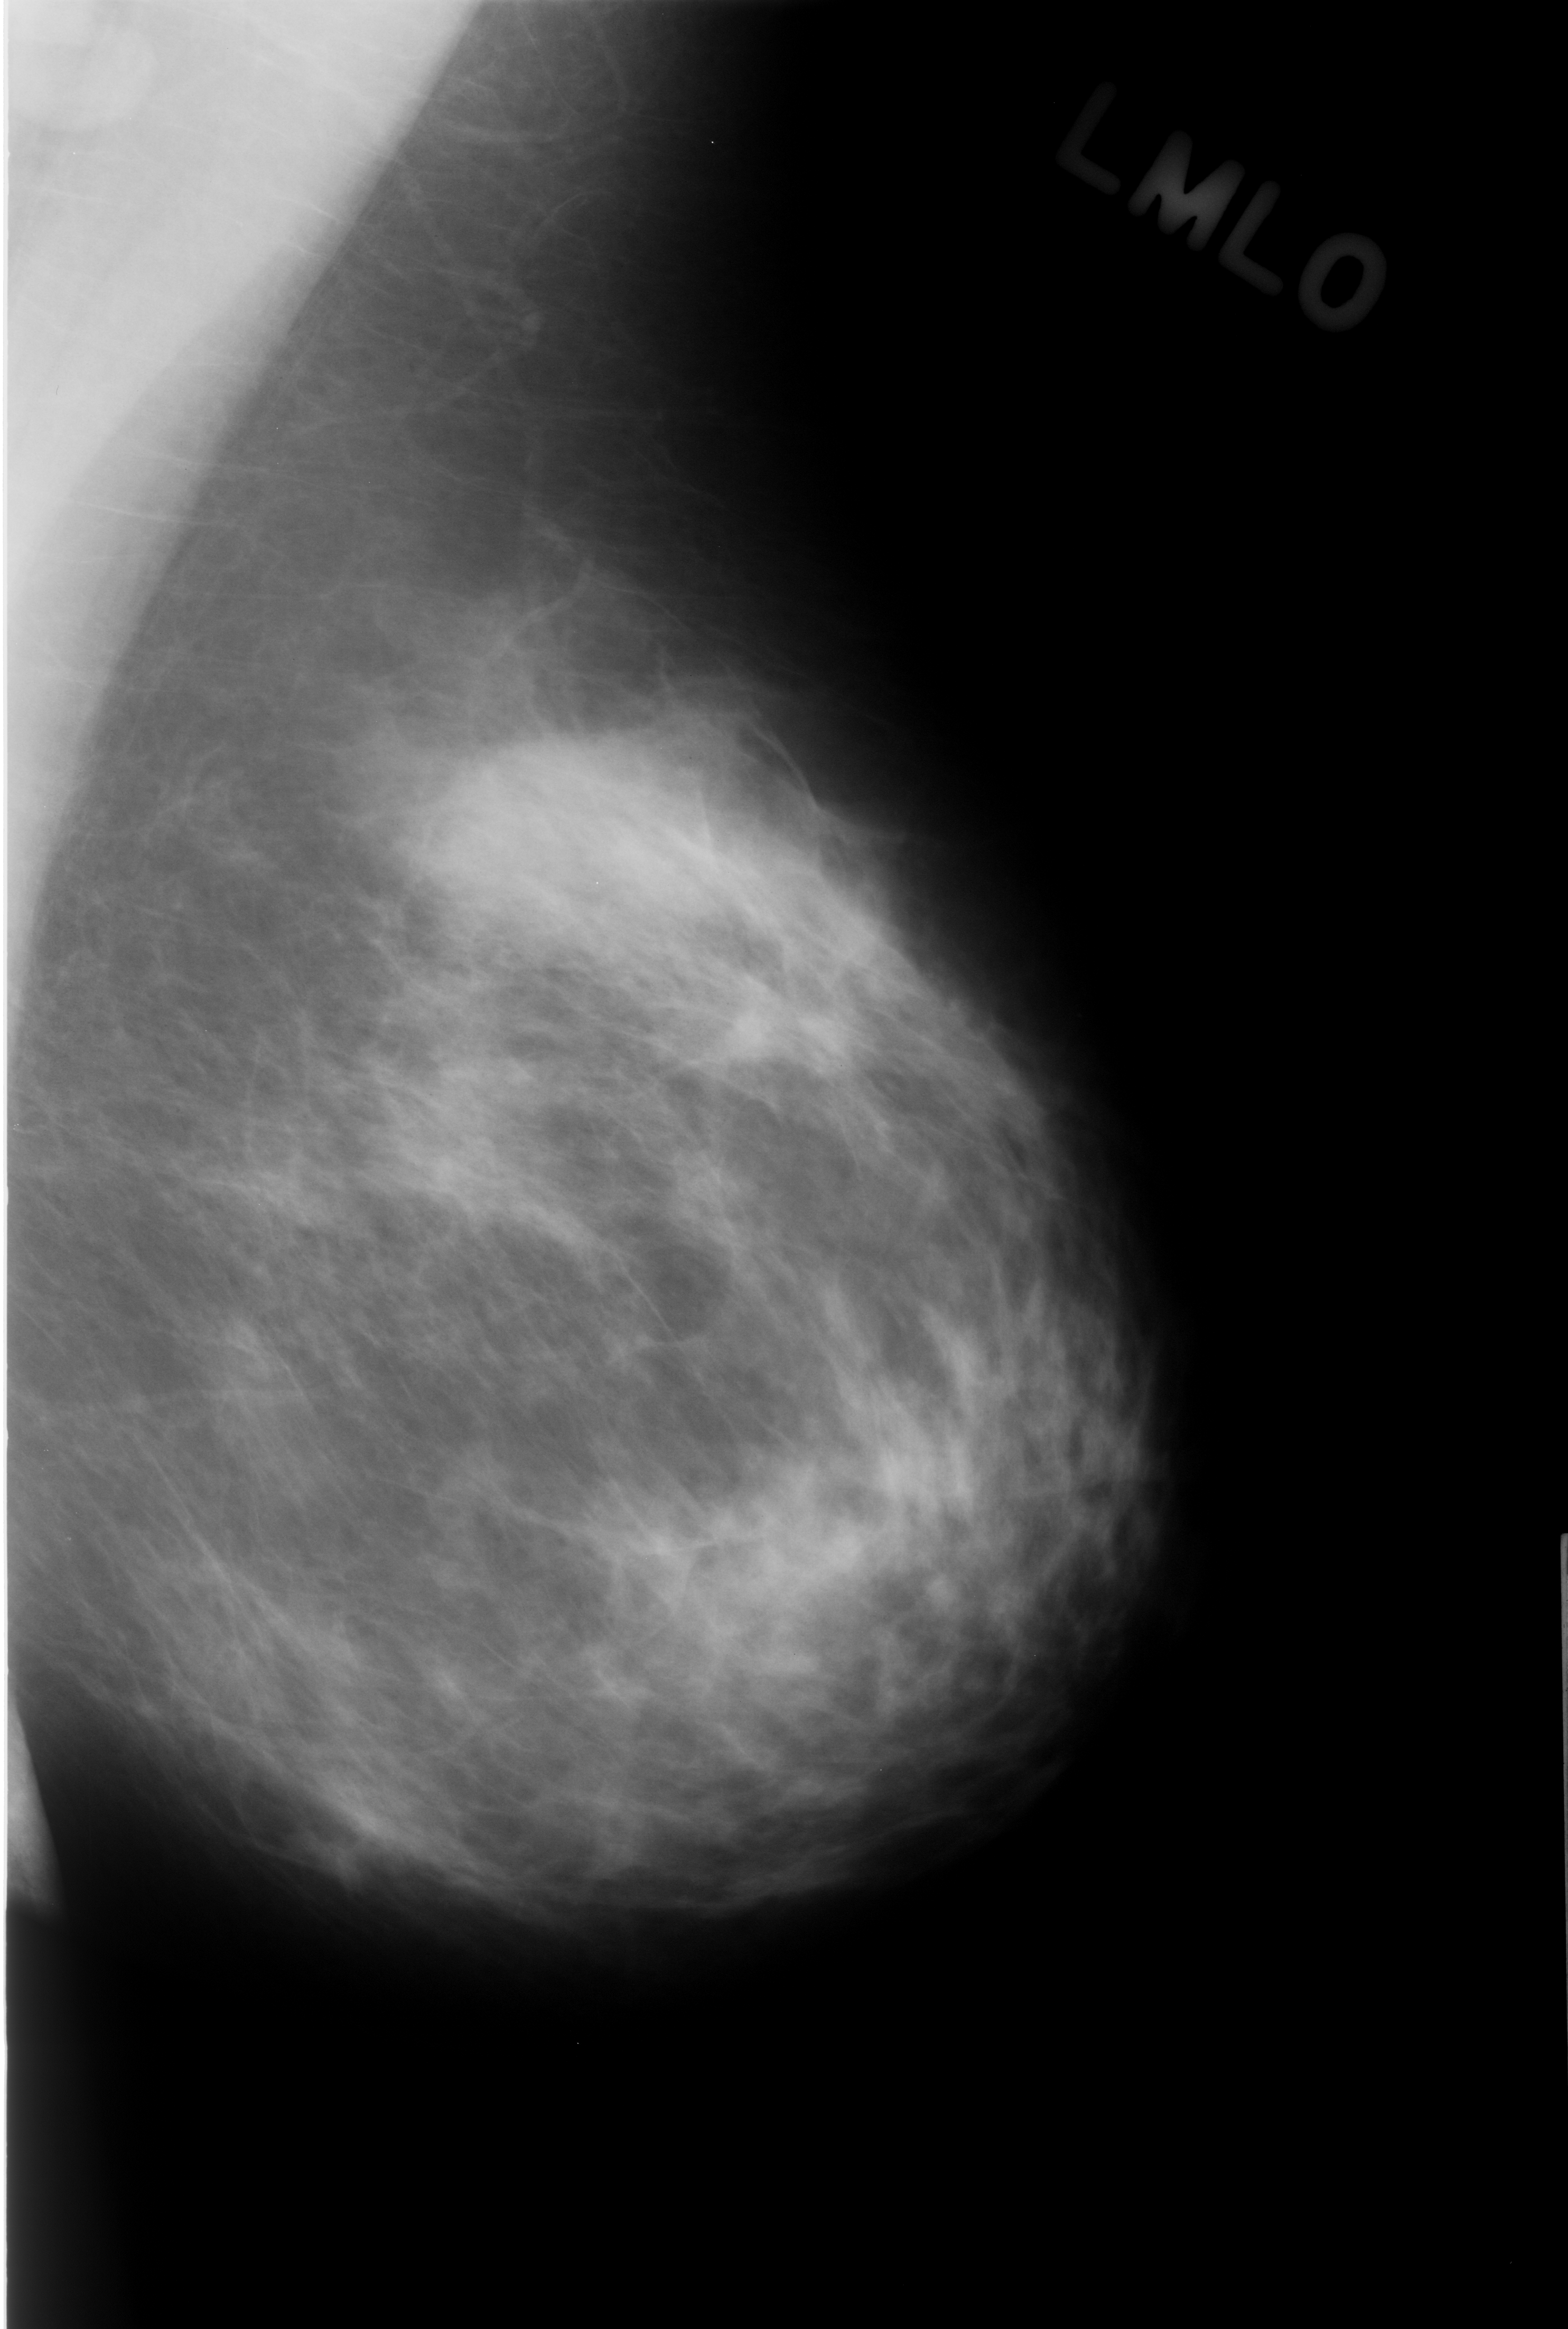
Digitized screen-film mammogram. Left breast. Mediolateral oblique (MLO) view. Breast composition: scattered fibroglandular densities (BI-RADS density category 2 of 4). 1568 × 2329 image matrix.
Expert-marked regions of interest on this film, with their recorded descriptors:
- mass, shape asymmetric breast tissue; BI-RADS assessment category 3; subtlety rating 5 on a 1 (subtle) to 5 (obvious) scale; benign; no additional work-up was recommended (outcome (as recorded, no biopsy): benign without callback): bounding box [x1, y1, x2, y2] px = [370, 664, 782, 1005]